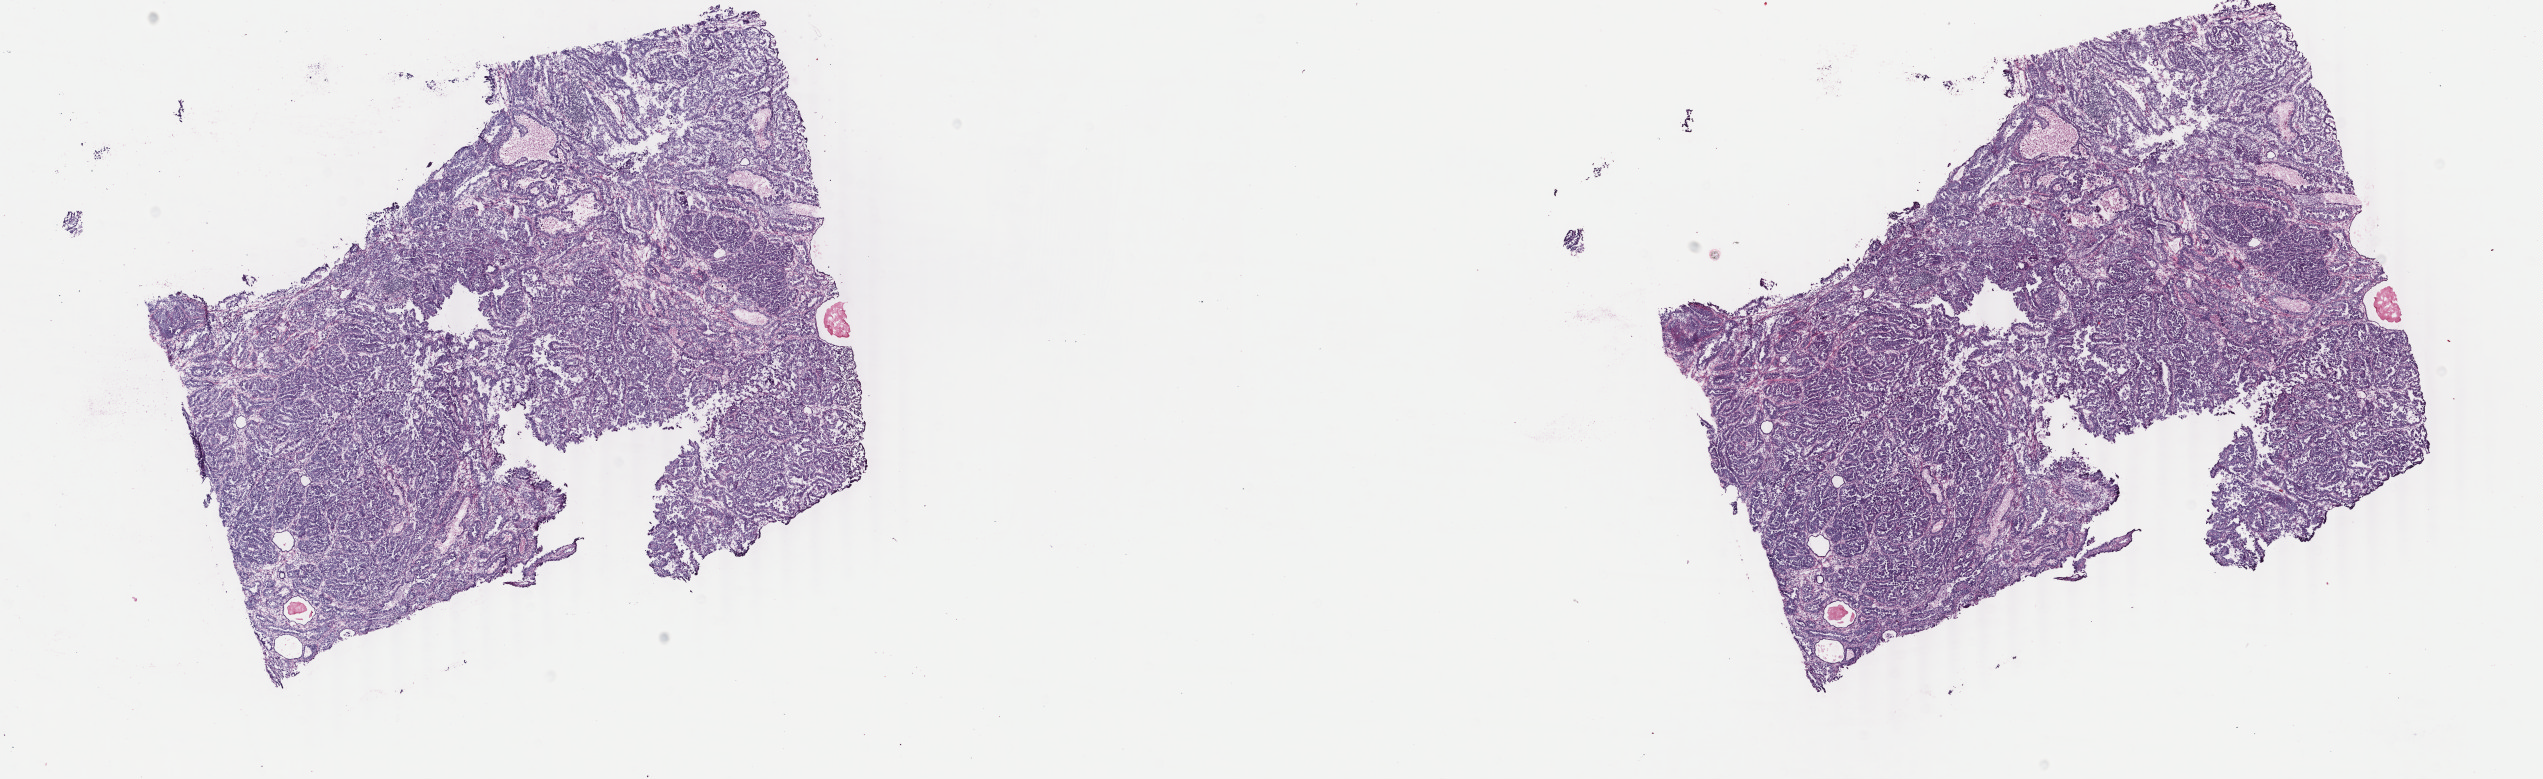
Whole-slide histology image, H&E — low-resolution overview of the scanned area, about 20.2 x 6.2 mm (acquisition: 40x scan); frozen section from the bottom of the tissue portion; primary tumour sample from the uterus. Female patient; age at initial diagnosis 71 years. Histologic grade: G3 (poorly differentiated). Slide review estimates, as recorded: tumour cells 80%, tumour nuclei 90%, normal cells 0%, stromal cells 10%, necrosis 10%. Inflammatory infiltration, as recorded: lymphocyte infiltration 10%, monocyte infiltration 0%, neutrophil infiltration 0%.
Diagnosis: Serous cystadenocarcinoma, NOS (endometrium). FIGO stage: IB.